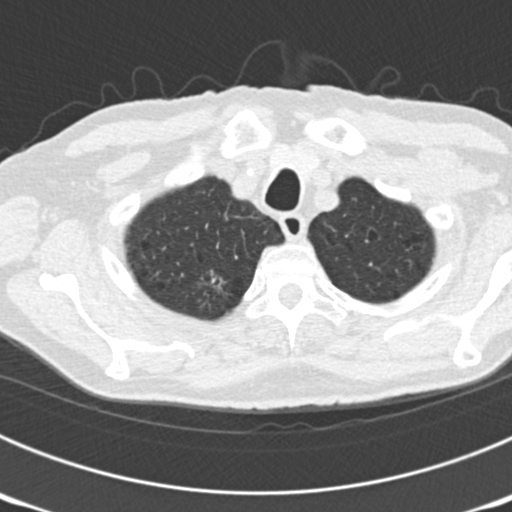
Low-dose screening chest CT, one axial slice; position 159 of 177 along the scan axis; reconstruction kernel B30f; 120 kVp; lung window (W 1500 / L -600 HU); 2 mm slice thickness; 512 × 512 image matrix, field of view 300 × 300 mm.
Annotated regions visible in this slice (manually delineated by an expert):
- lesion 3 (nodule, upper lobe of right lung): bounding box [x1, y1, x2, y2] px = [202, 269, 225, 290]